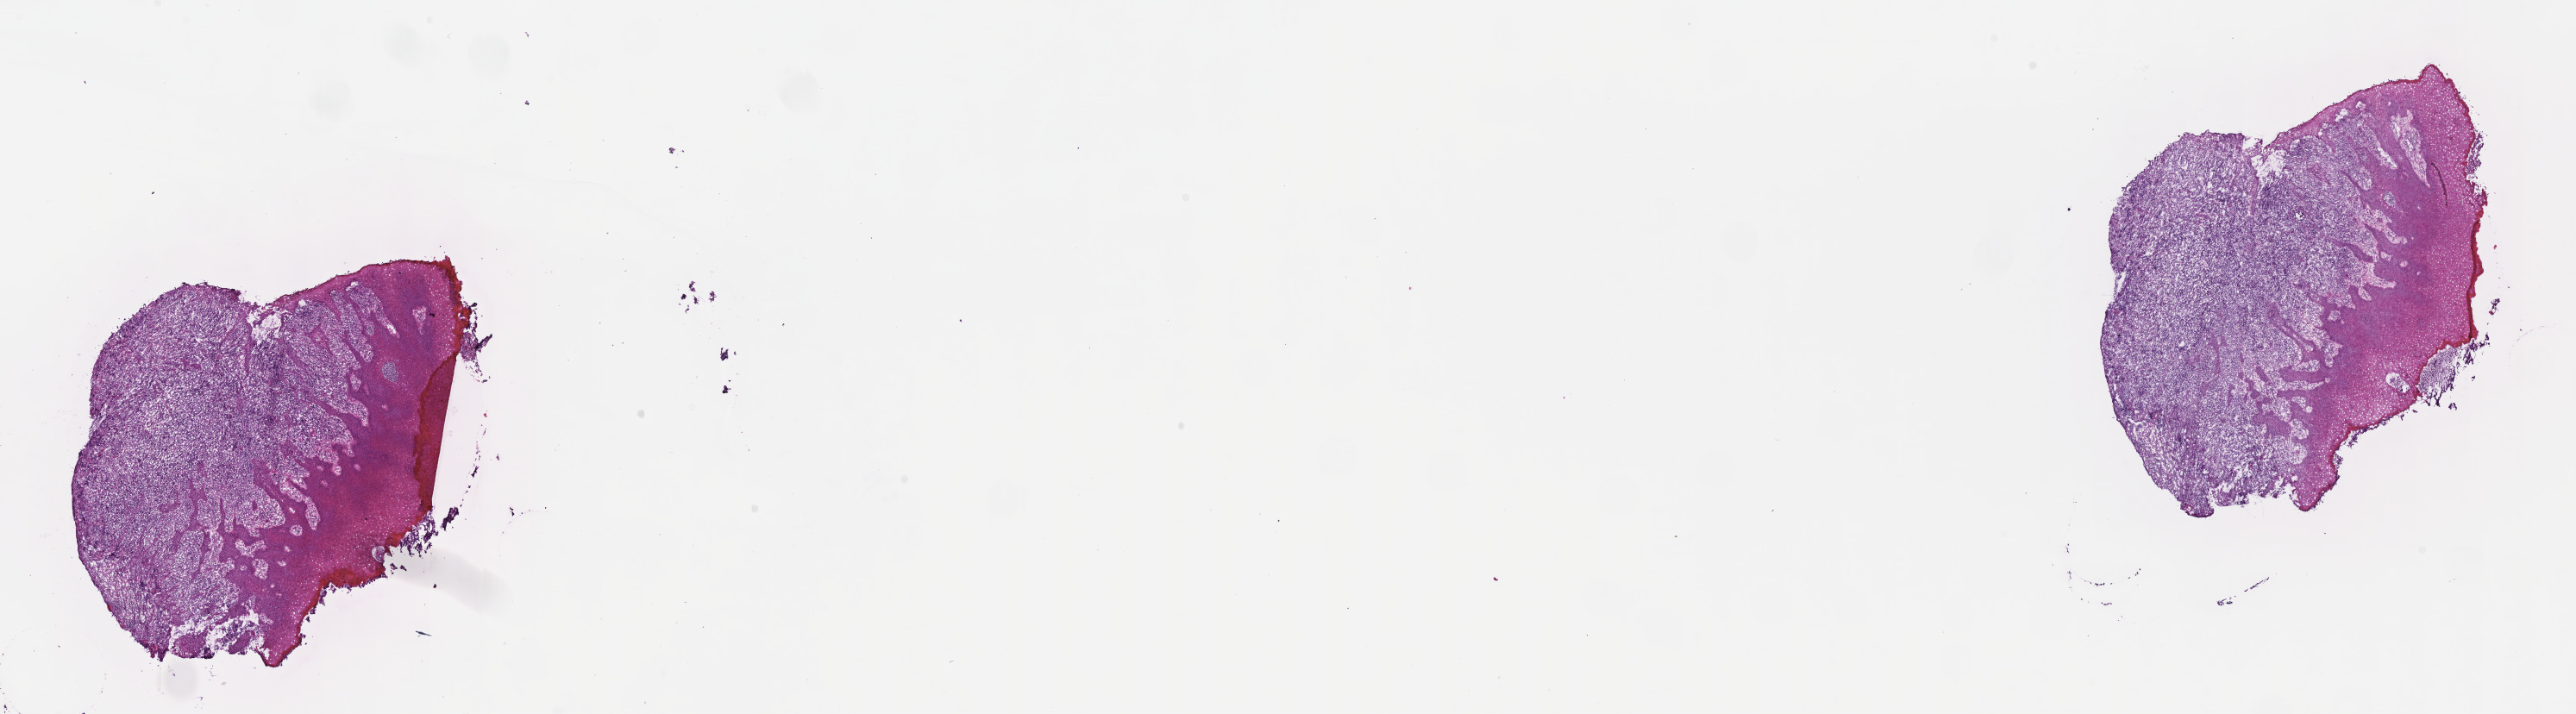
Whole-slide image, hematoxylin and eosin (H&E) stain — a low-resolution overview of the entire scanned area, about 24.2 x 6.7 mm; frozen section (tissue freezing medium); primary tumor; anatomic site: mandible. Male, age 9 years at initial diagnosis. Pathologist review of this section (percent, as recorded): tumor cells 50%, tumor nuclei 50%, stromal cells 50%, necrosis 0%, normal cells 0%. Inflammatory infiltration, as recorded: lymphocyte infiltration 5%, monocyte infiltration 15%, neutrophil infiltration 5%.
Ann Arbor stage (patient): Stage III. Histologic diagnosis: Burkitt lymphoma, NOS.